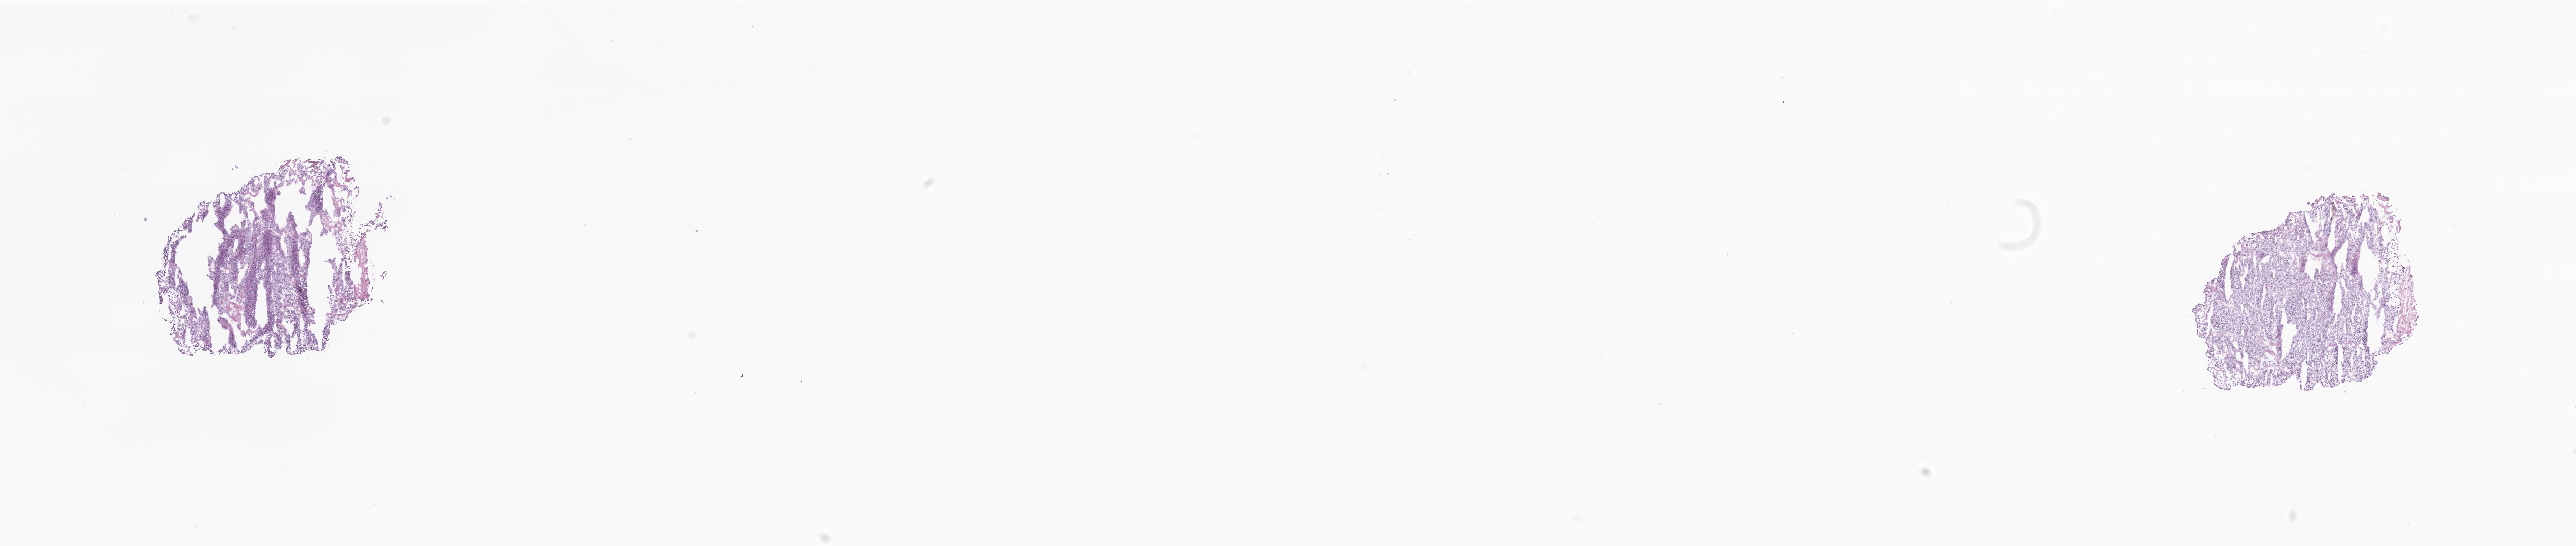
Haematoxylin and eosin whole-slide image, shown as a low-resolution overview of the whole scanned area (about 30.4 x 6.5 mm), frozen section, specimen: primary tumor, anatomic site: breast. Patient: female, age at initial diagnosis 86 years. Pathologist review of this section (percent, as recorded): tumor cells 85%, tumor nuclei 85%.
Histologic diagnosis: Infiltrating duct carcinoma, NOS.